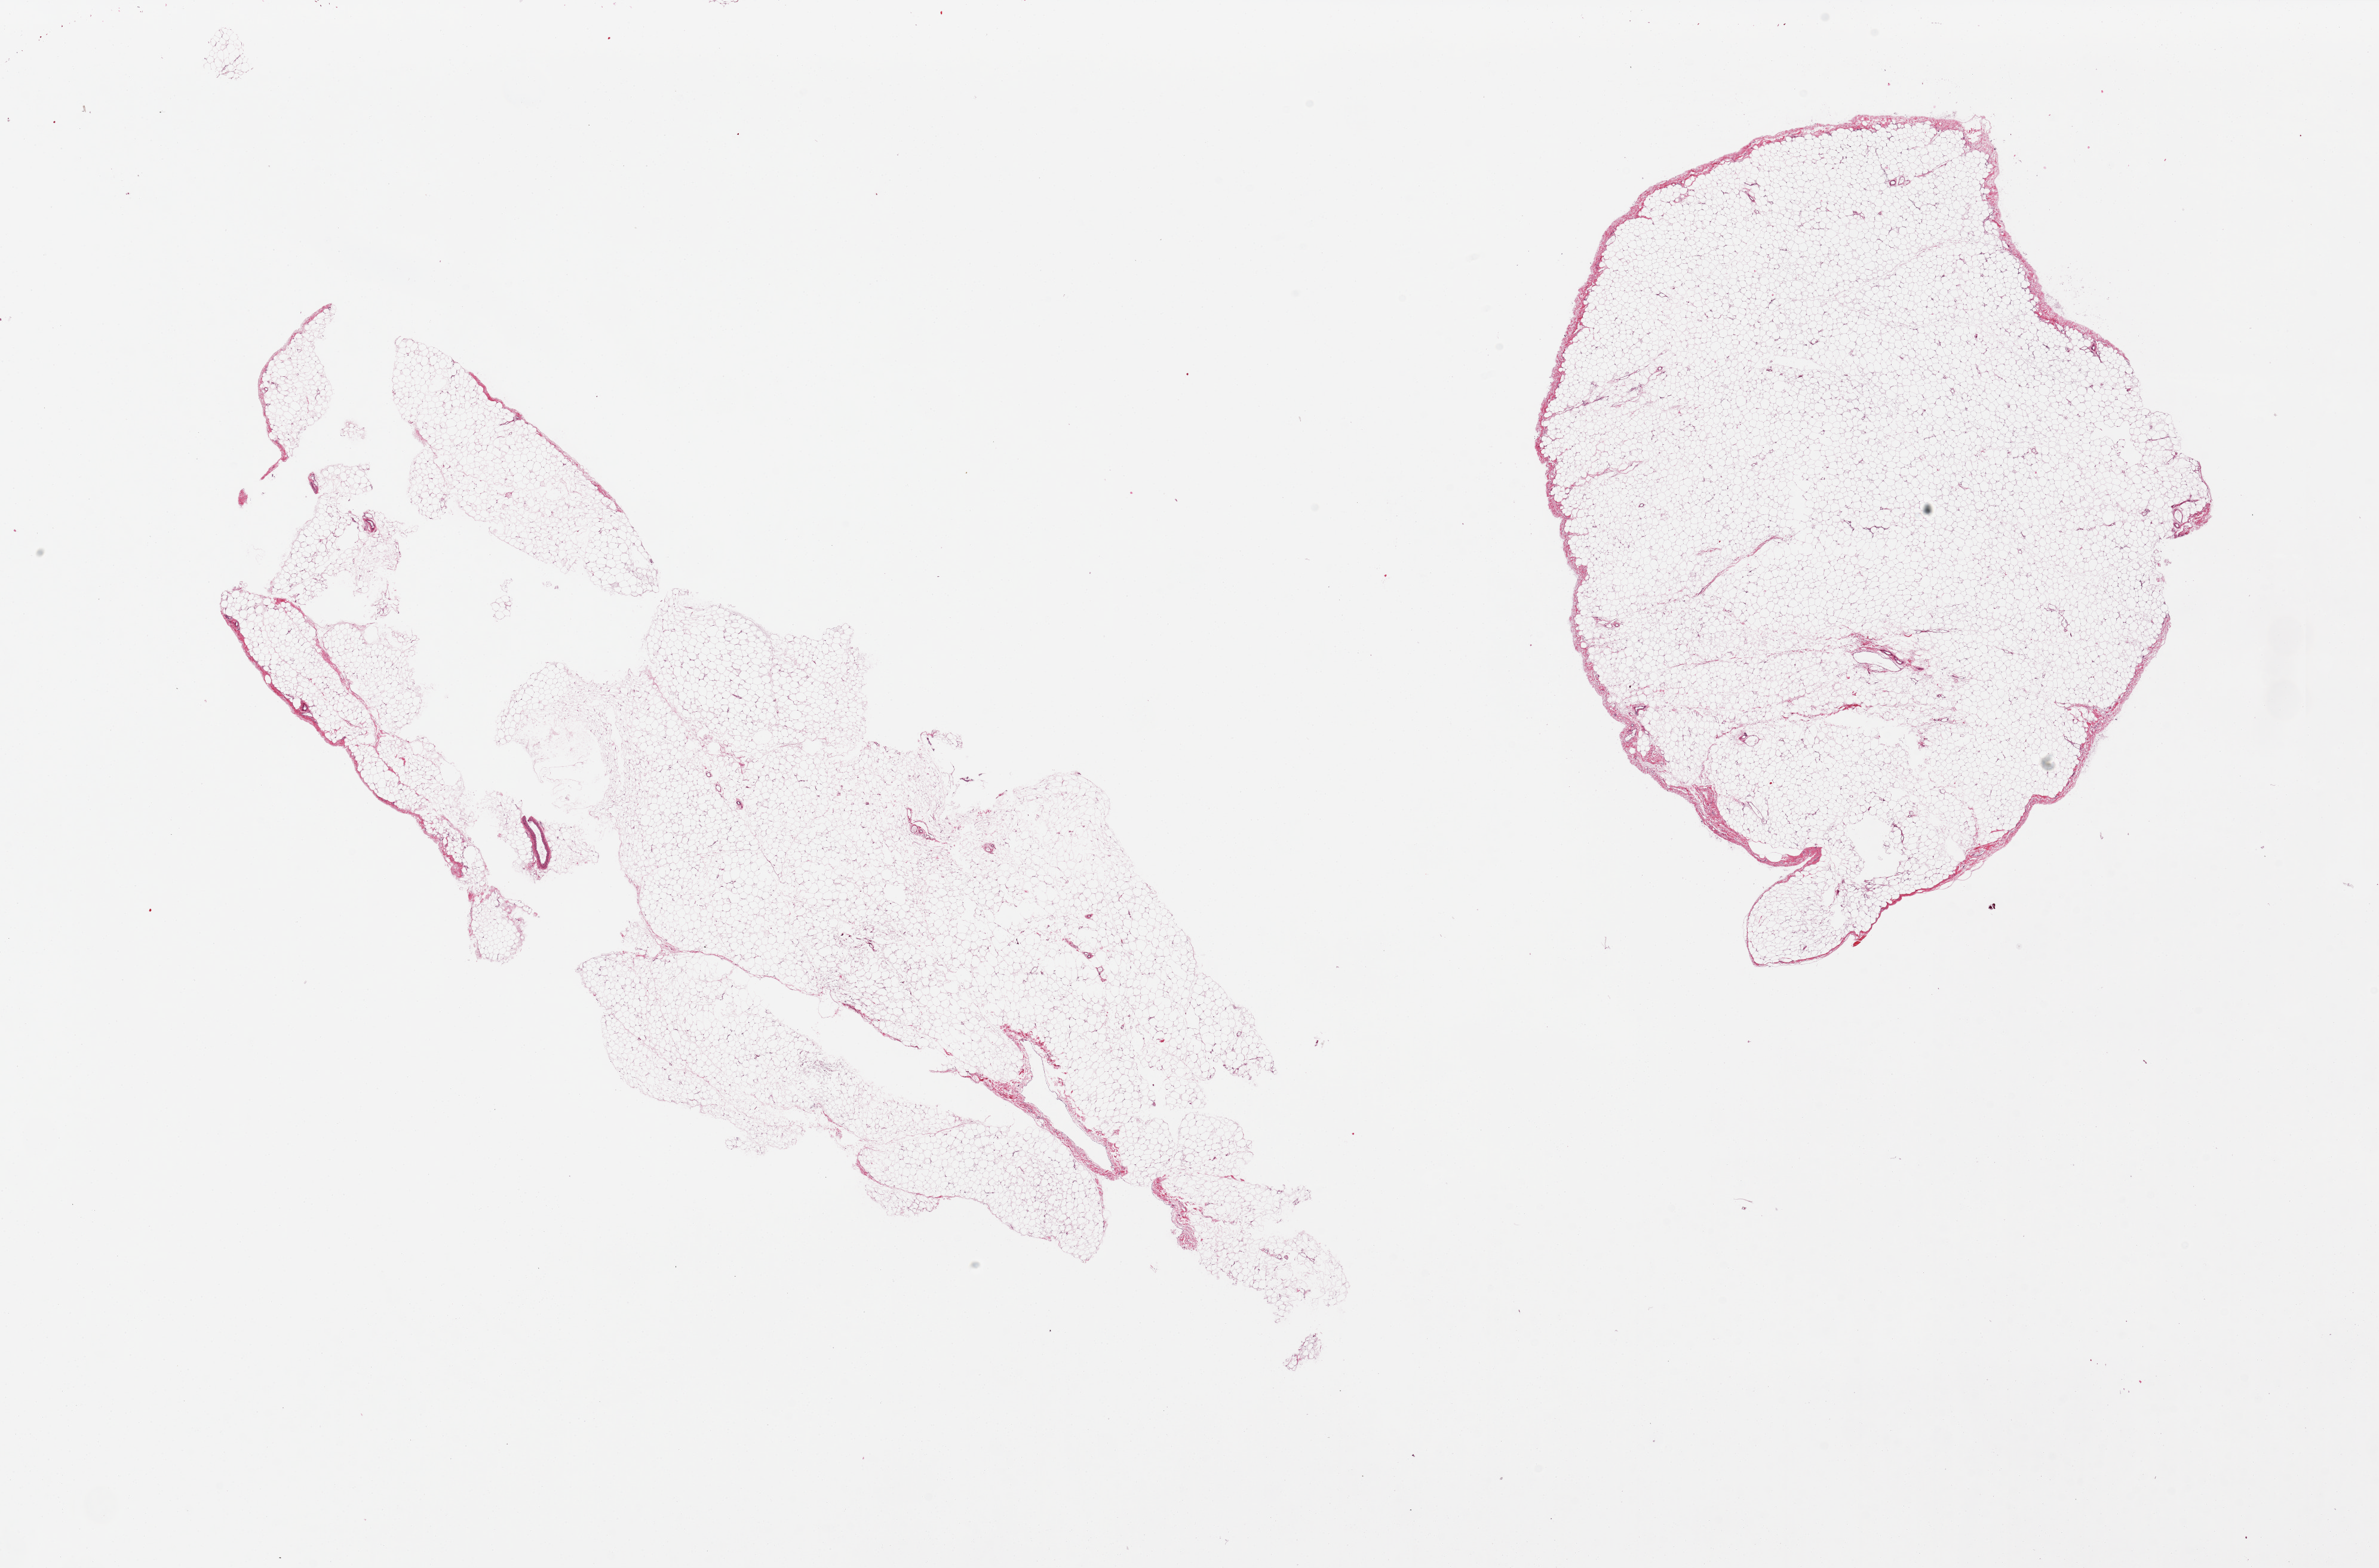
Digitized hematoxylin and eosin (H&E)-stained section, brightfield, a low-resolution overview of the entire scanned area, about 31.5 x 20.8 mm (slide scanned at 20x), PAXgene-fixed, paraffin-embedded tissue, section of omentum (target tissue), tissue donor sample. Male donor.
- review note (as recorded): 2 pieces; central hole in one piece; few small vessels